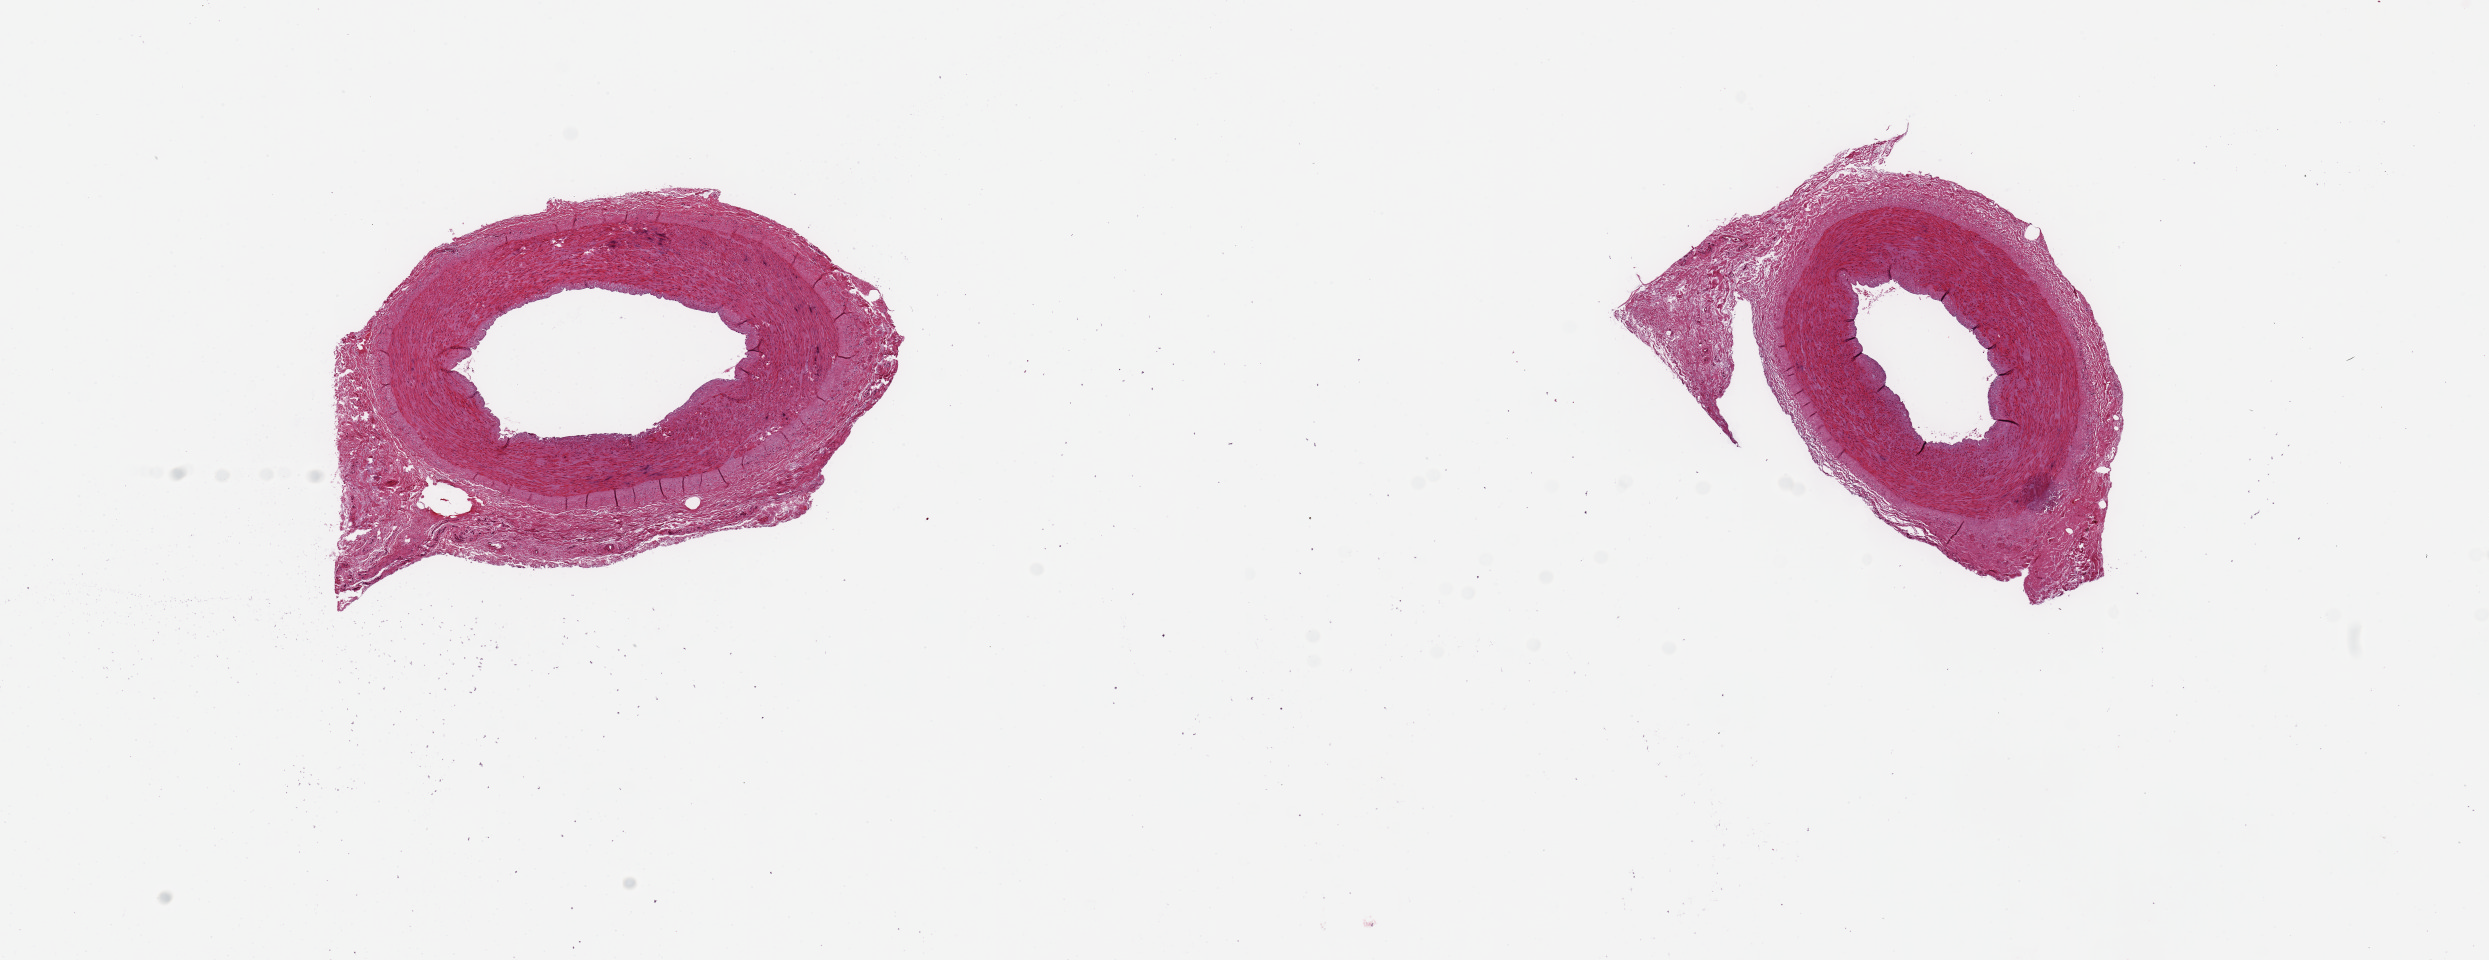
Digitized H&E-stained section, whole scanned area (about 19.7 x 7.6 mm, acquisition: 20x scan) shown as a low-resolution overview, PAXgene-fixed, paraffin-embedded tissue, sampled site (target tissue): tibial artery, donor tissue sample. Donor: male.
Pathologist's review note for this sample: 2 pieces ~2.5mm d; Fibroconnective circumferential layer `~0.5mm.